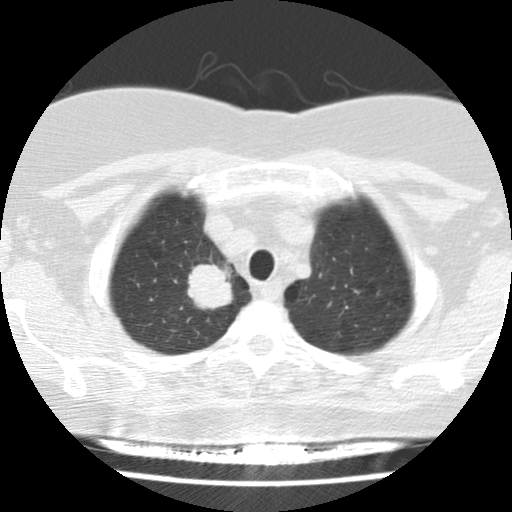
Chest CT (low-dose screening protocol), one axial image. Baseline screening round. Lung window (W 1500 / L -600 HU). Standard (soft-tissue) reconstruction kernel (STANDARD). 512 × 512 image matrix. Female, age 58 years at enrolment. Former smoker at enrolment.
Expert-annotated lung lesion, bounding box (x1, y1, x2, y2) in pixels: (169, 247, 247, 325). The exam's reader record, not a measurement of the box and not confirmed to be the same lesion: non-calcified nodule or mass ≥4 mm, right upper lobe, 28 × 24 mm, spiculated (stellate) margins, soft tissue attenuation. Official screen result: positive, change unspecified: nodule(s) >= 4 mm or enlarging nodule(s), mass(es), or other non-specific abnormalities suspicious for lung cancer. Later outcome: lung cancer diagnosed 40 days after this screen — adenocarcinoma, NOS, right upper lobe, poorly differentiated (G3), stage IB (AJCC 6th edition), 29 mm at pathology.